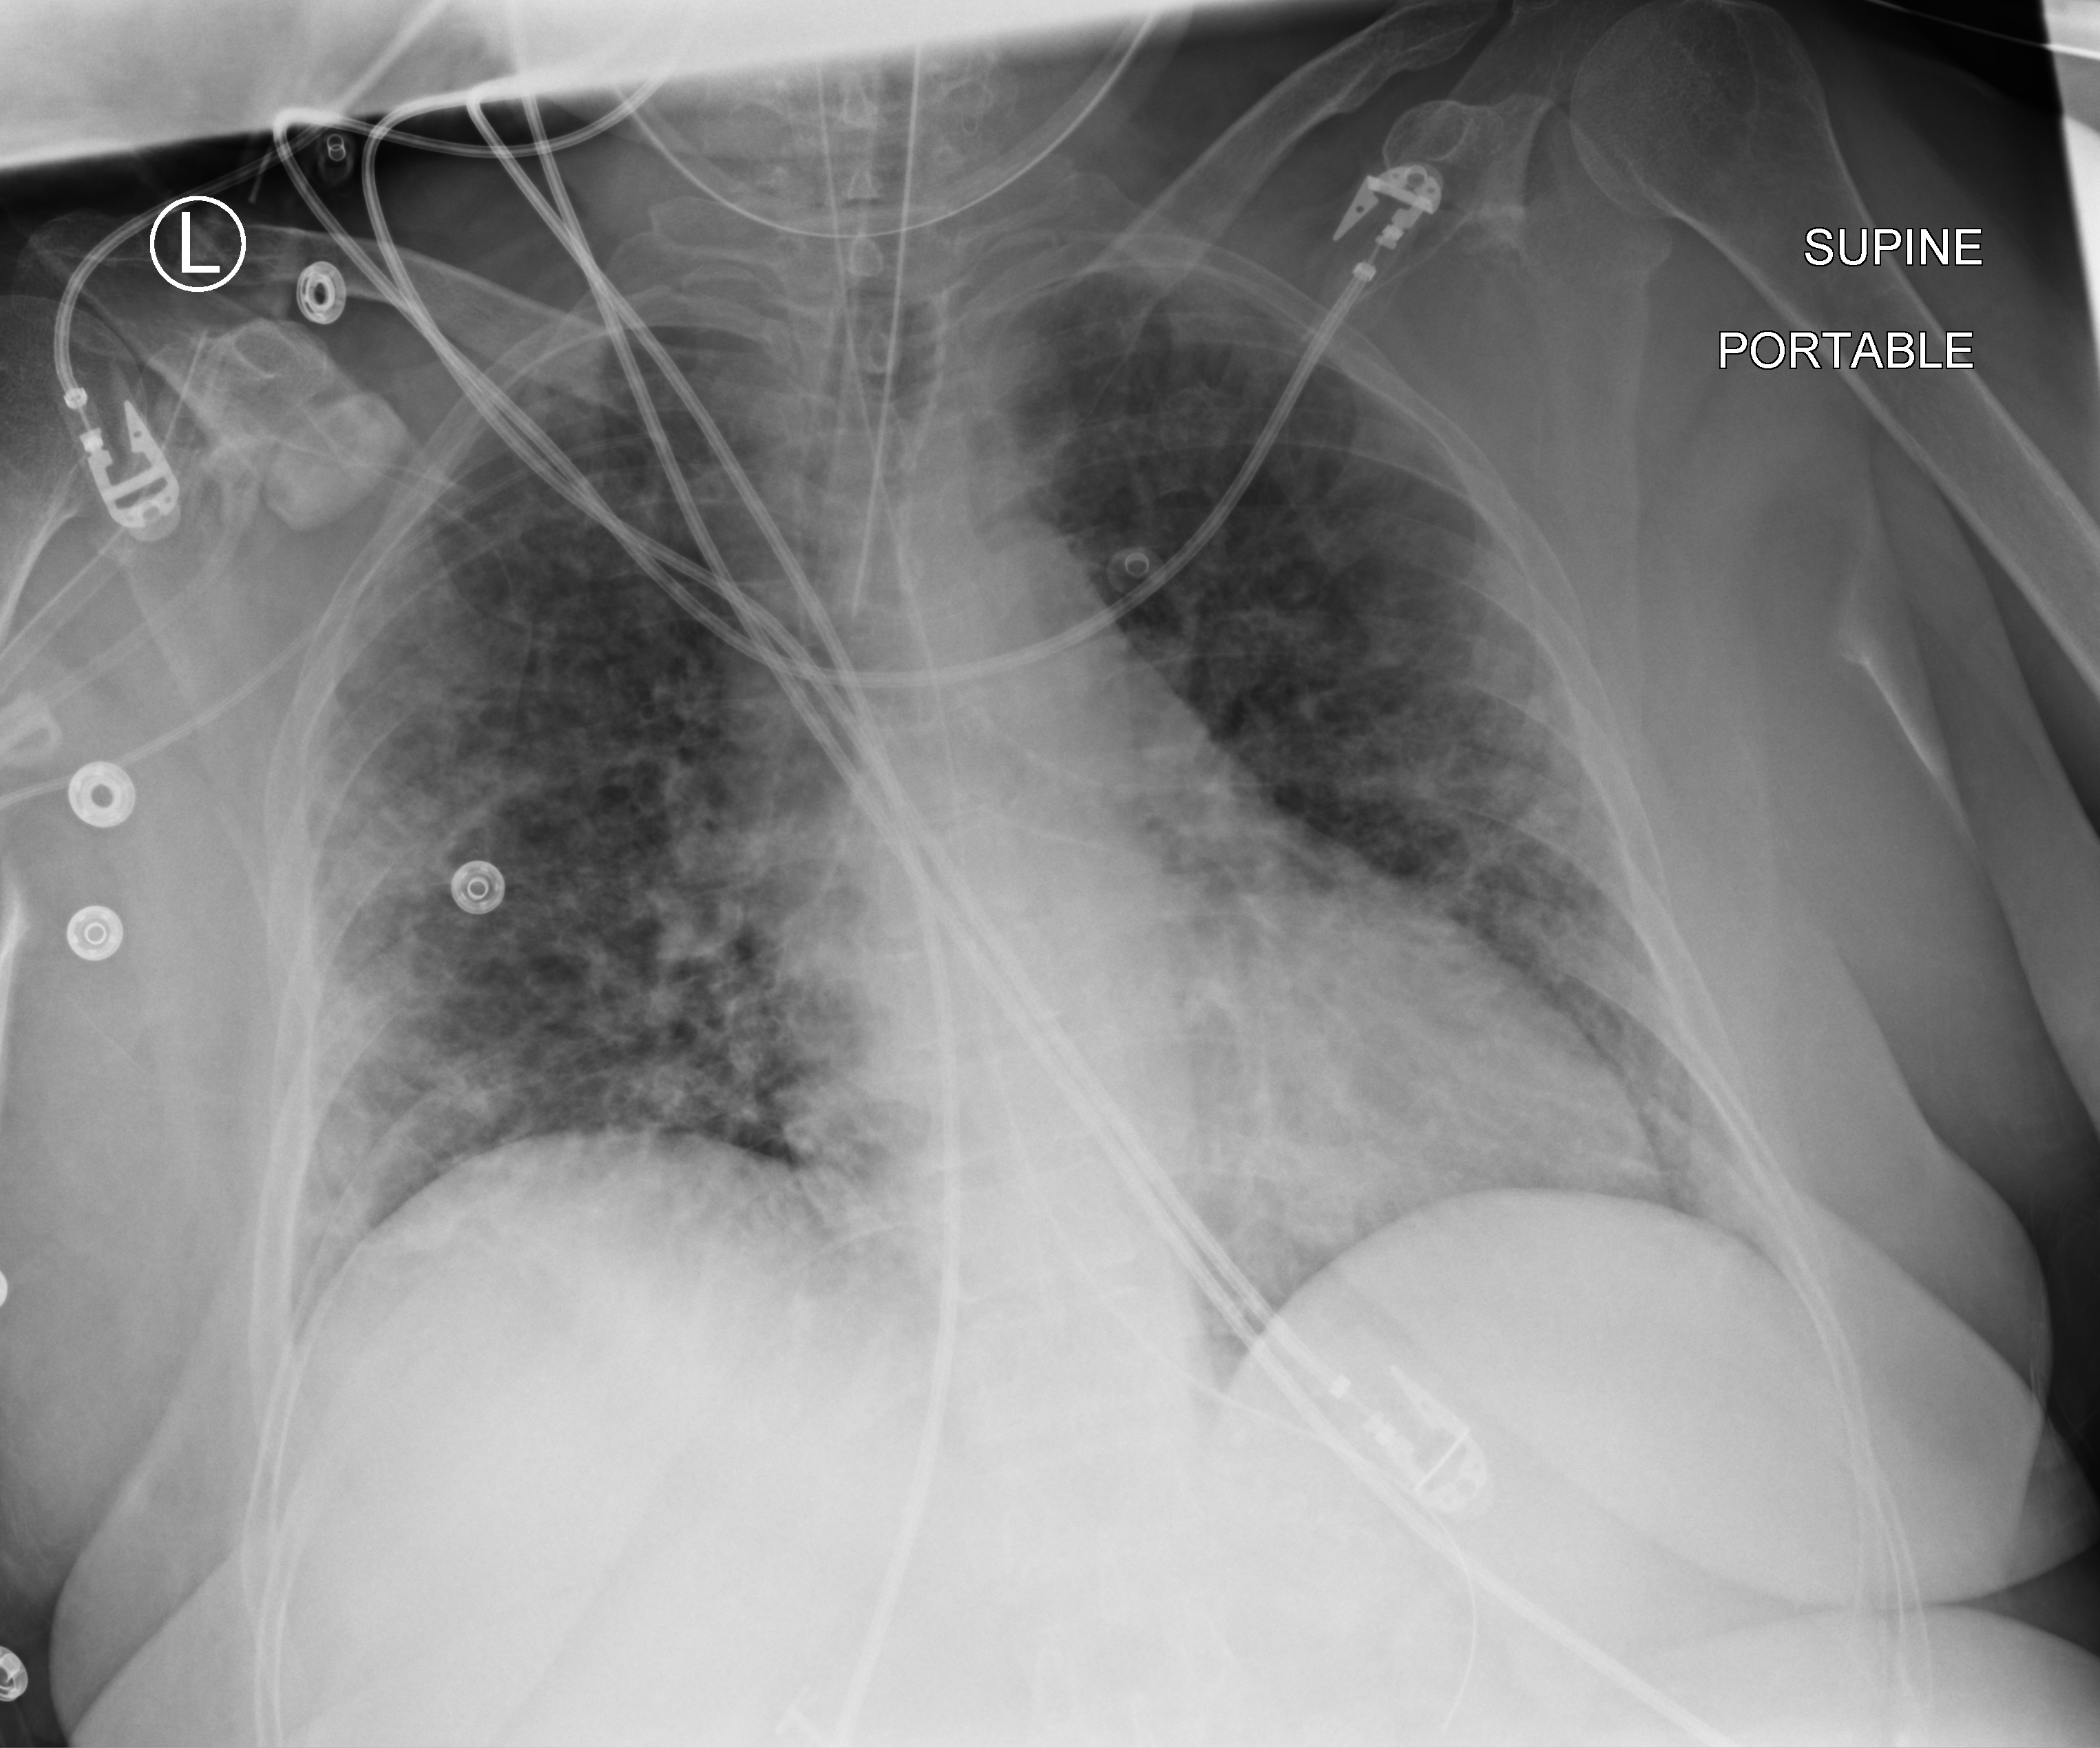
Chest X-ray (portable), anteroposterior (AP) projection. Female patient hospitalised with COVID-19, age 18–59 years.
From the hospital-stay record, not from the radiograph (when in the stay this image was taken is not recorded):
- mechanically ventilated during this hospital stay: yes
- admitted to intensive care during this hospital stay: yes
- length of hospital stay: 22 days